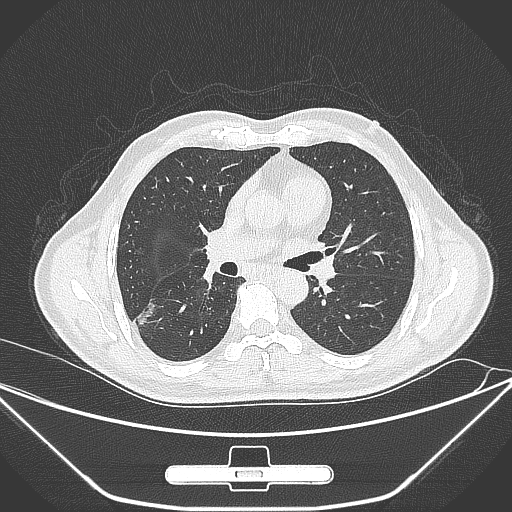
Chest CT, one axial slice. Slice 158 of 310 in the series (ordered by position). 120 kVp. Lung window (W 1500 / L -600 HU). 1 mm slice thickness. 512 × 512 image matrix, field of view 398 × 398 mm. Patient: male, 71 years. From the clinical record (not read from this slice): clinical TNM (as recorded): T1c N0 M0.
Annotated regions visible in this slice (bounding box drawn by a radiologist):
- lung tumour (recorded histology: adenocarcinoma): box from (x=137, y=301) to (x=156, y=326) px